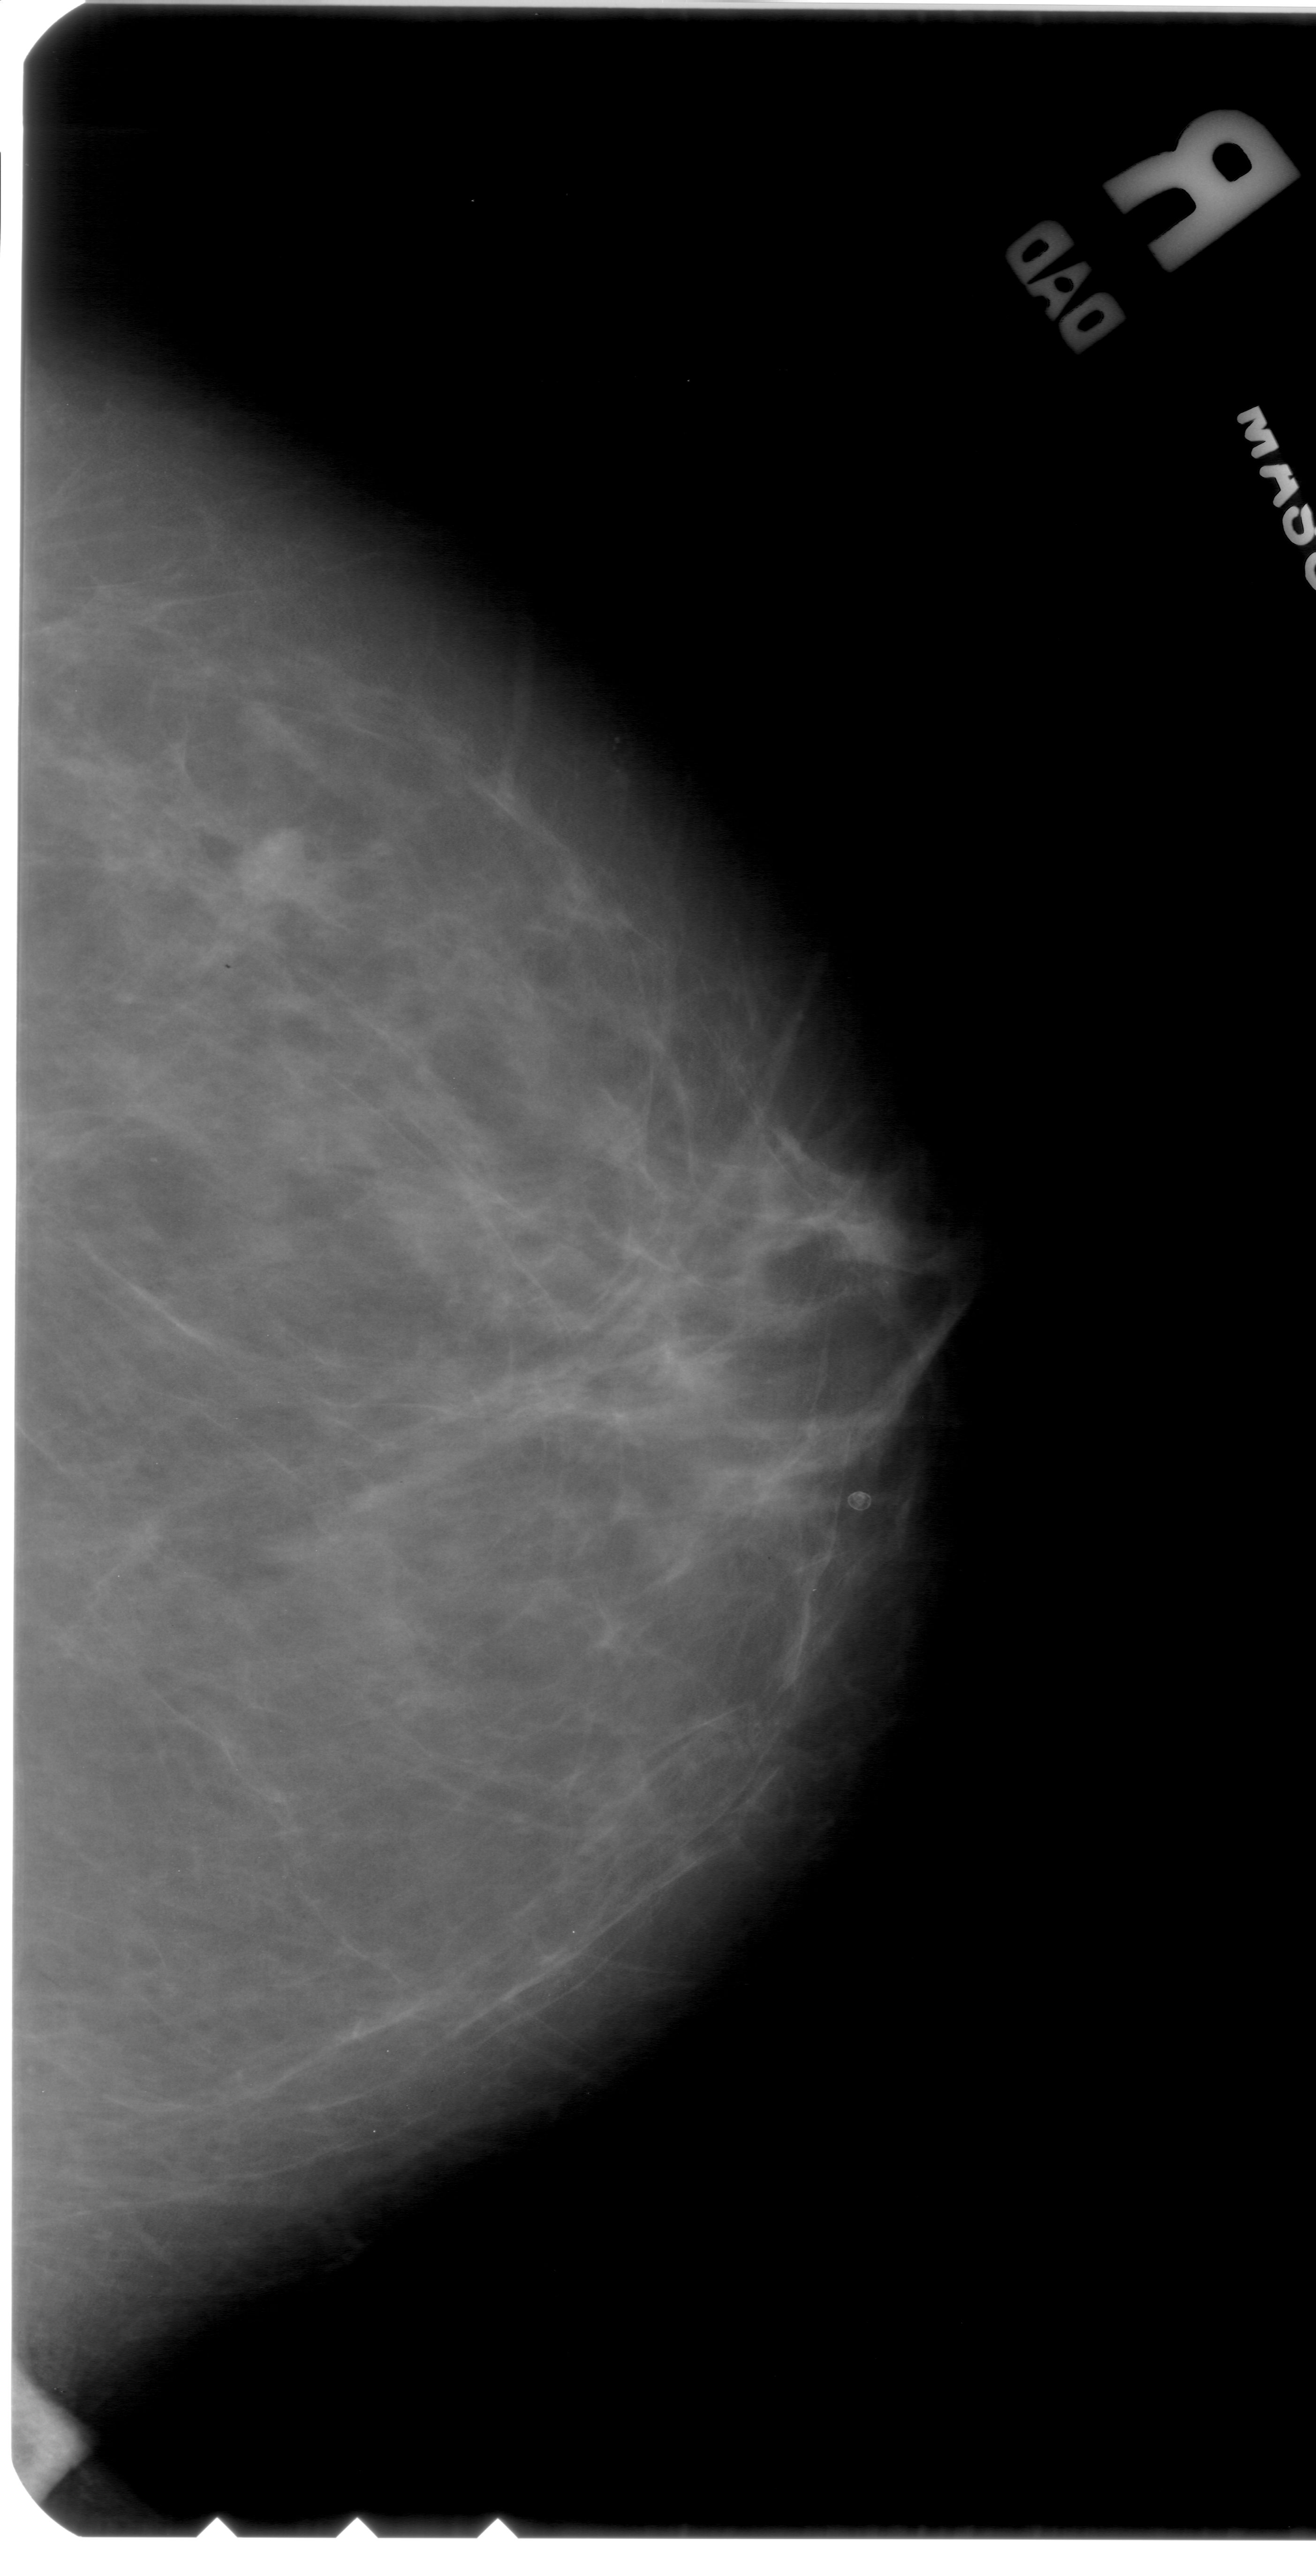
Scanned film-screen mammogram; right breast; craniocaudal (CC) view; BI-RADS breast density category 2 (scale 1–4); 1316 × 2576 image matrix.
Marked abnormalities (boxes around the expert regions of interest):
- mass, shape lobulated, margins obscured; BI-RADS assessment category 4; subtlety rating 2 on a 1 (subtle) to 5 (obvious) scale; pathology result (as recorded, not read from the image): malignant: bounding box <232,820,314,897> (left, top, right, bottom; pixels)